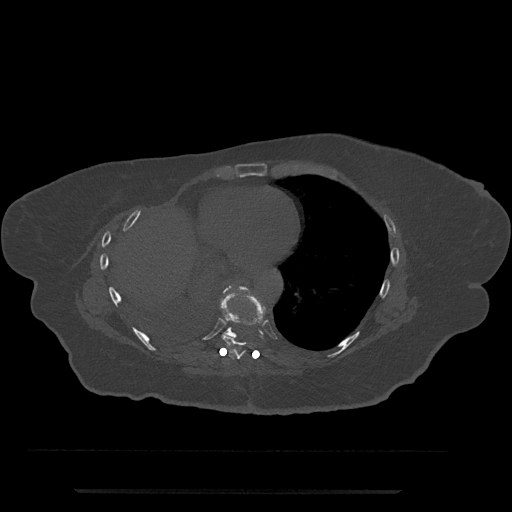
CT including the spine, one axial slice; position 375 of 797 along the scan axis; 120 kVp; bone window (W 1800 / L 400 HU); 512 × 512 image matrix. Female patient, age 51 years. From the clinical record (not read from this slice): primary cancer: neuro.
Outlined on this slice (semi-automatically segmented with operator editing):
- T8 vertebra: bounding box [x1, y1, x2, y2] px = [221, 292, 265, 359]
- T9 vertebra: [218, 284, 264, 339]